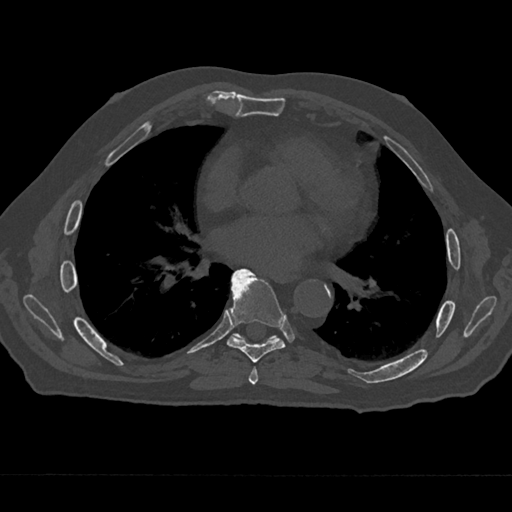
CT including the spine, one axial slice; slice 361 of 797 in the series (ordered by position); bone window (W 1800 / L 400 HU); 512 × 512 image matrix. Male patient, age 75 years. Case-level facts recorded for this patient, not image findings: primary cancer: renal.
Annotated regions visible in this slice (semi-automatic segmentation, software-assisted and operator-edited):
- T6 vertebra: bounding box [x1, y1, x2, y2] px = [249, 367, 258, 385]
- T7 vertebra: [227, 269, 286, 363]
- T8 vertebra: [232, 333, 277, 341]